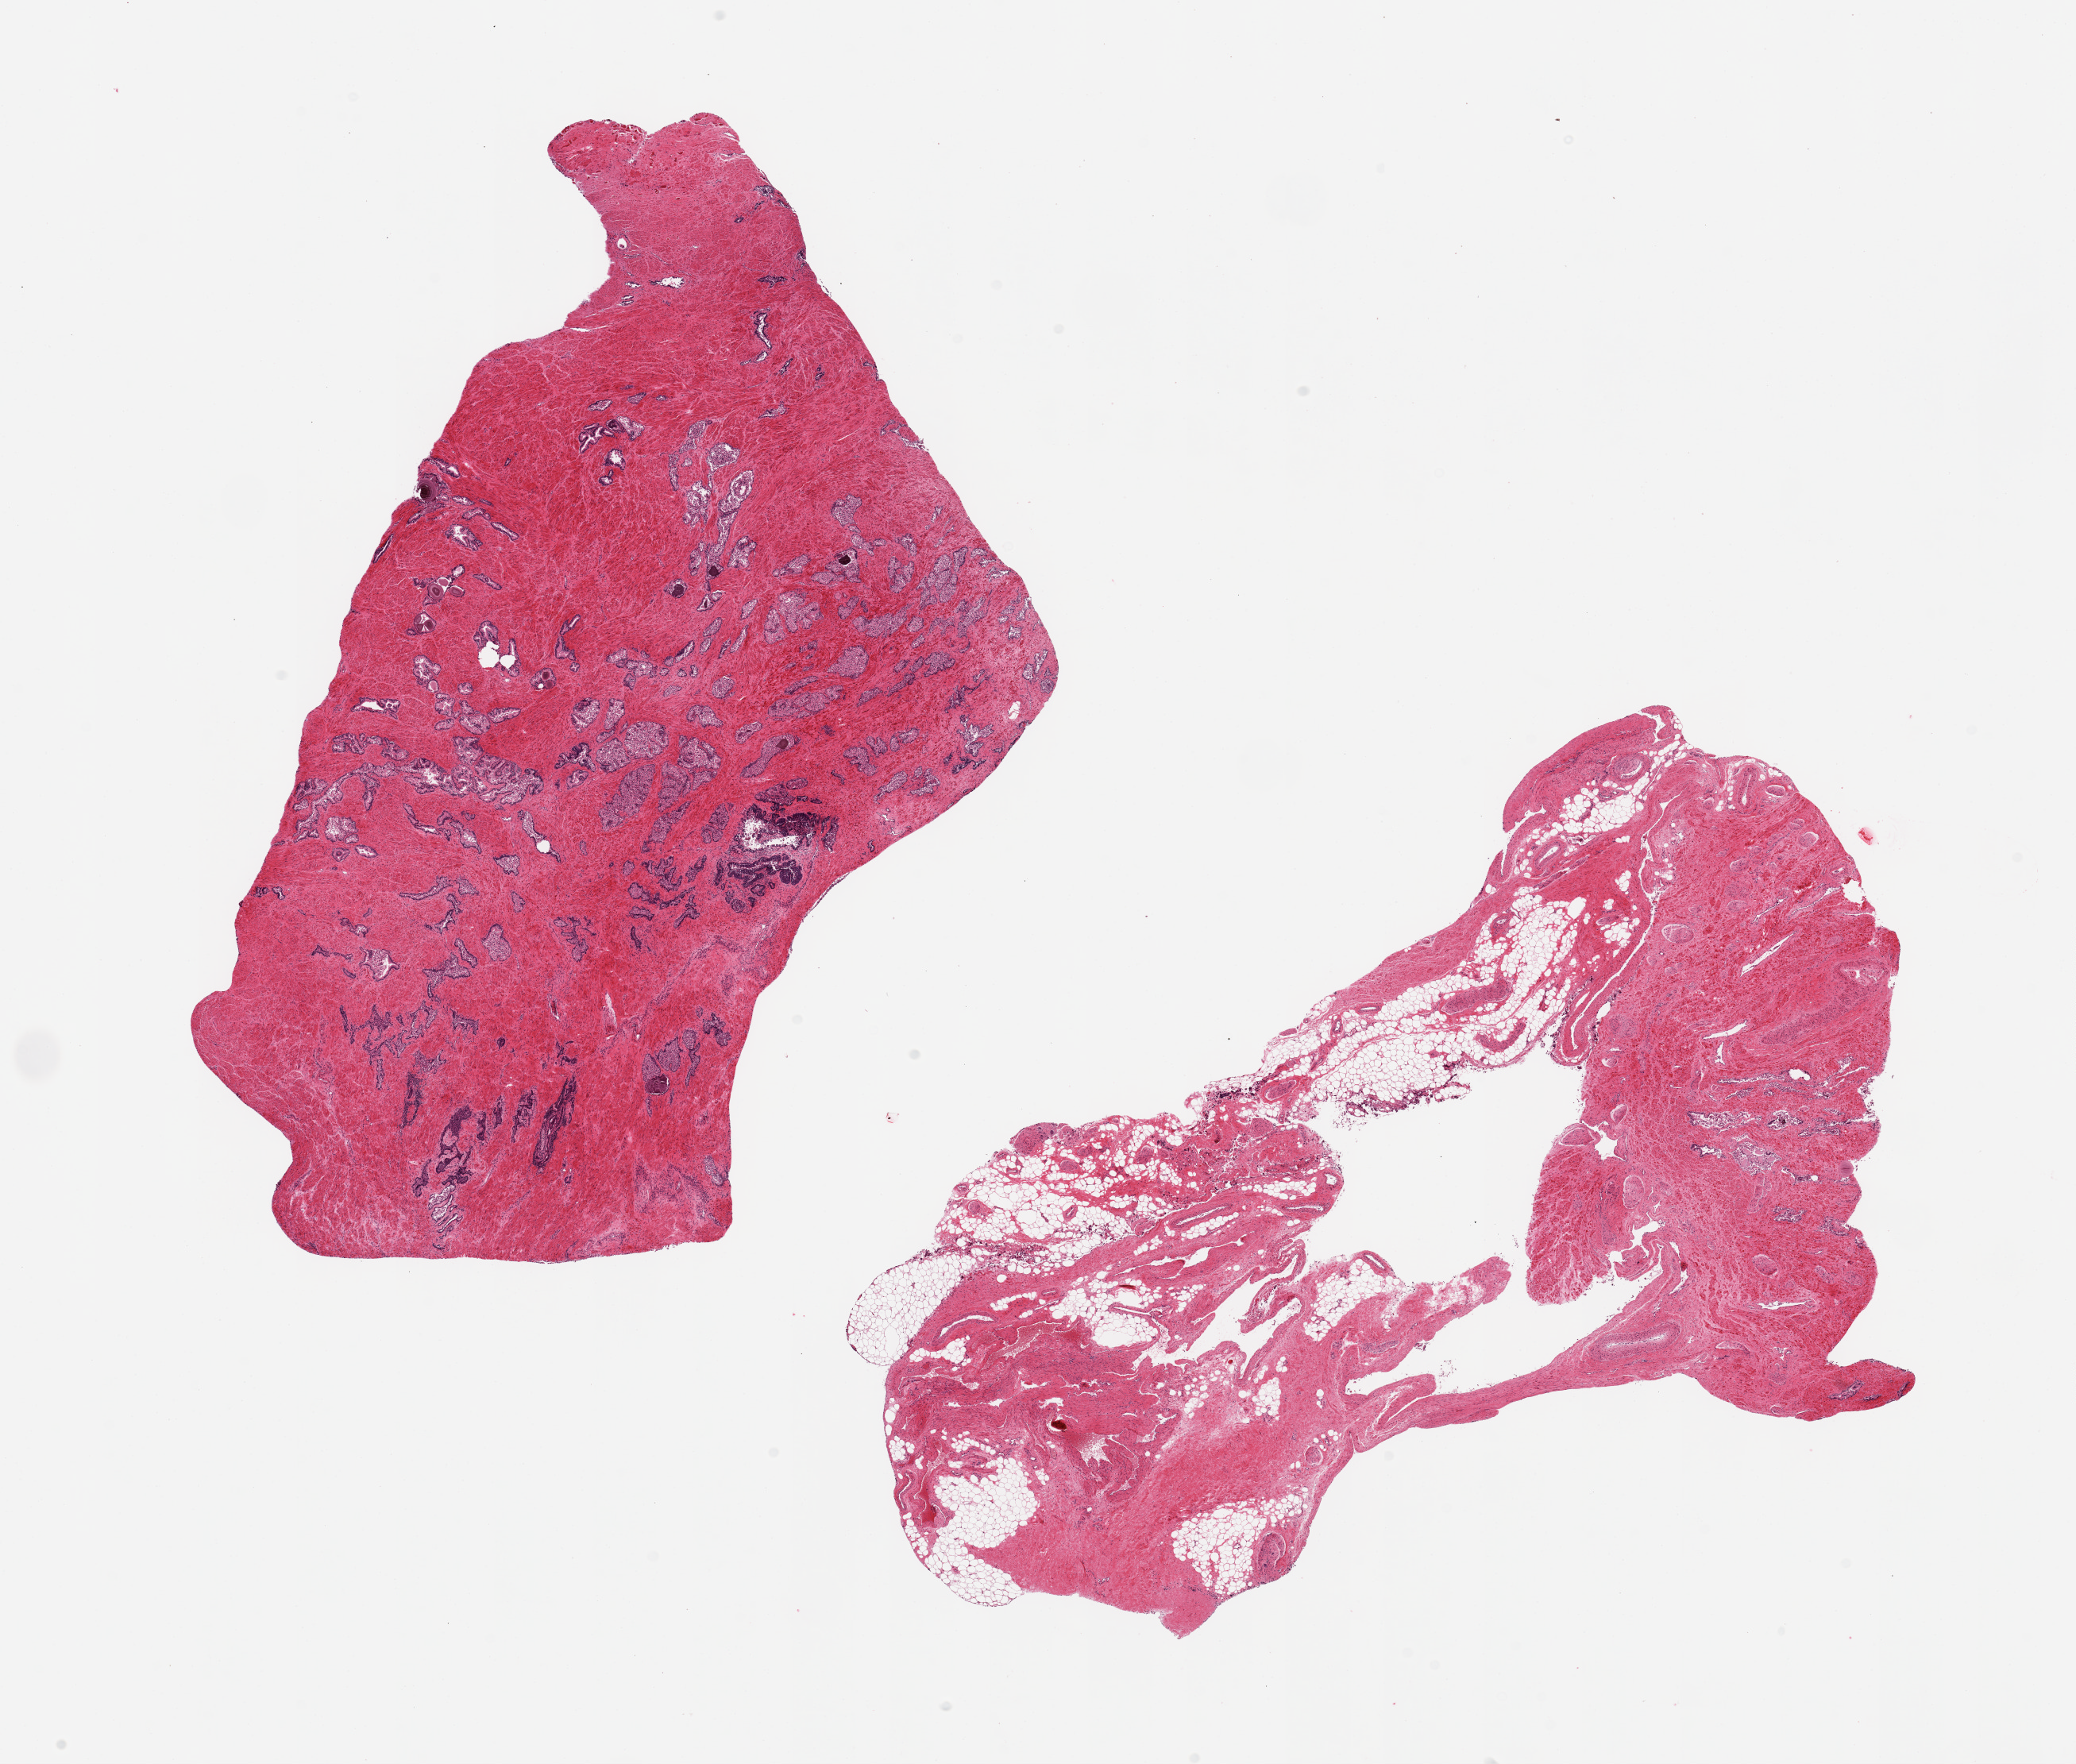
Digitized hematoxylin and eosin (H&E)-stained section, shown as a low-resolution overview of the whole scanned area (about 20.7 x 17.6 mm); PAXgene-fixed paraffin-embedded (PFPE) section; section of prostate (target tissue); donor tissue sample.
Review note (as recorded): 2 pieces; 1 piece is ~10% stroma and glands, 90% is fat, fibrovascular tissue, and nerve; second has focal prostatitis, glands largely sloughed.